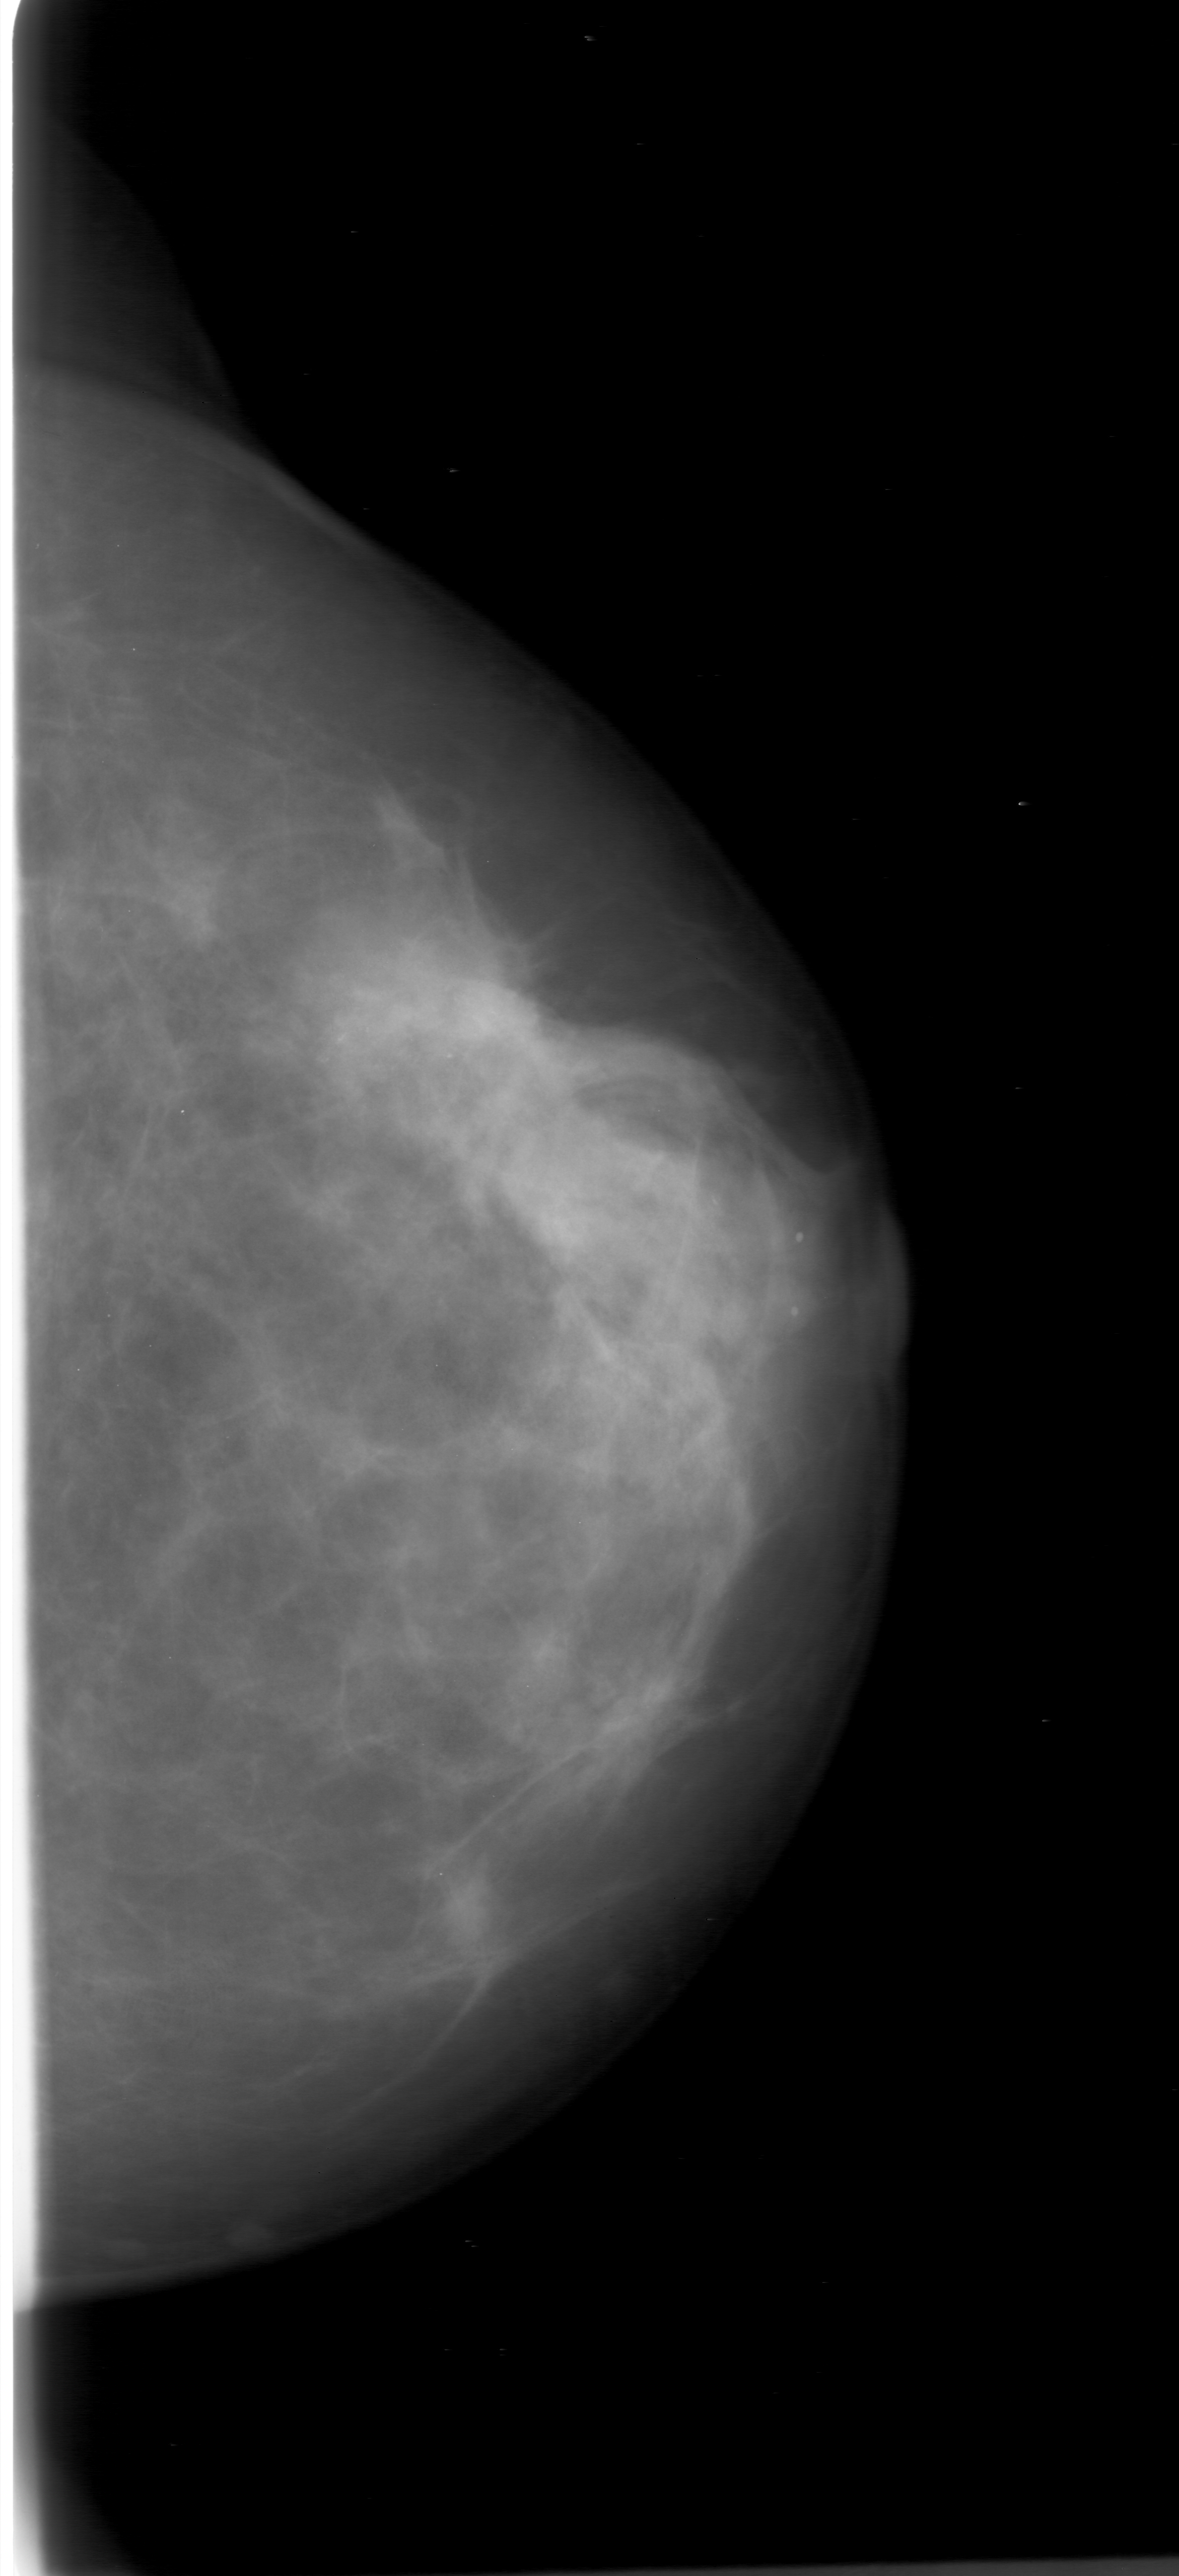
Digitized screen-film mammogram; left breast; CC view; BI-RADS breast density category 2 (scale 1–4).
- Marked abnormality: calcifications, morphology amorphous, distribution segmental; BI-RADS assessment category 4; subtlety rating 3 on a 1 (subtle) to 5 (obvious) scale; pathology result (as recorded, not read from the image): malignant.